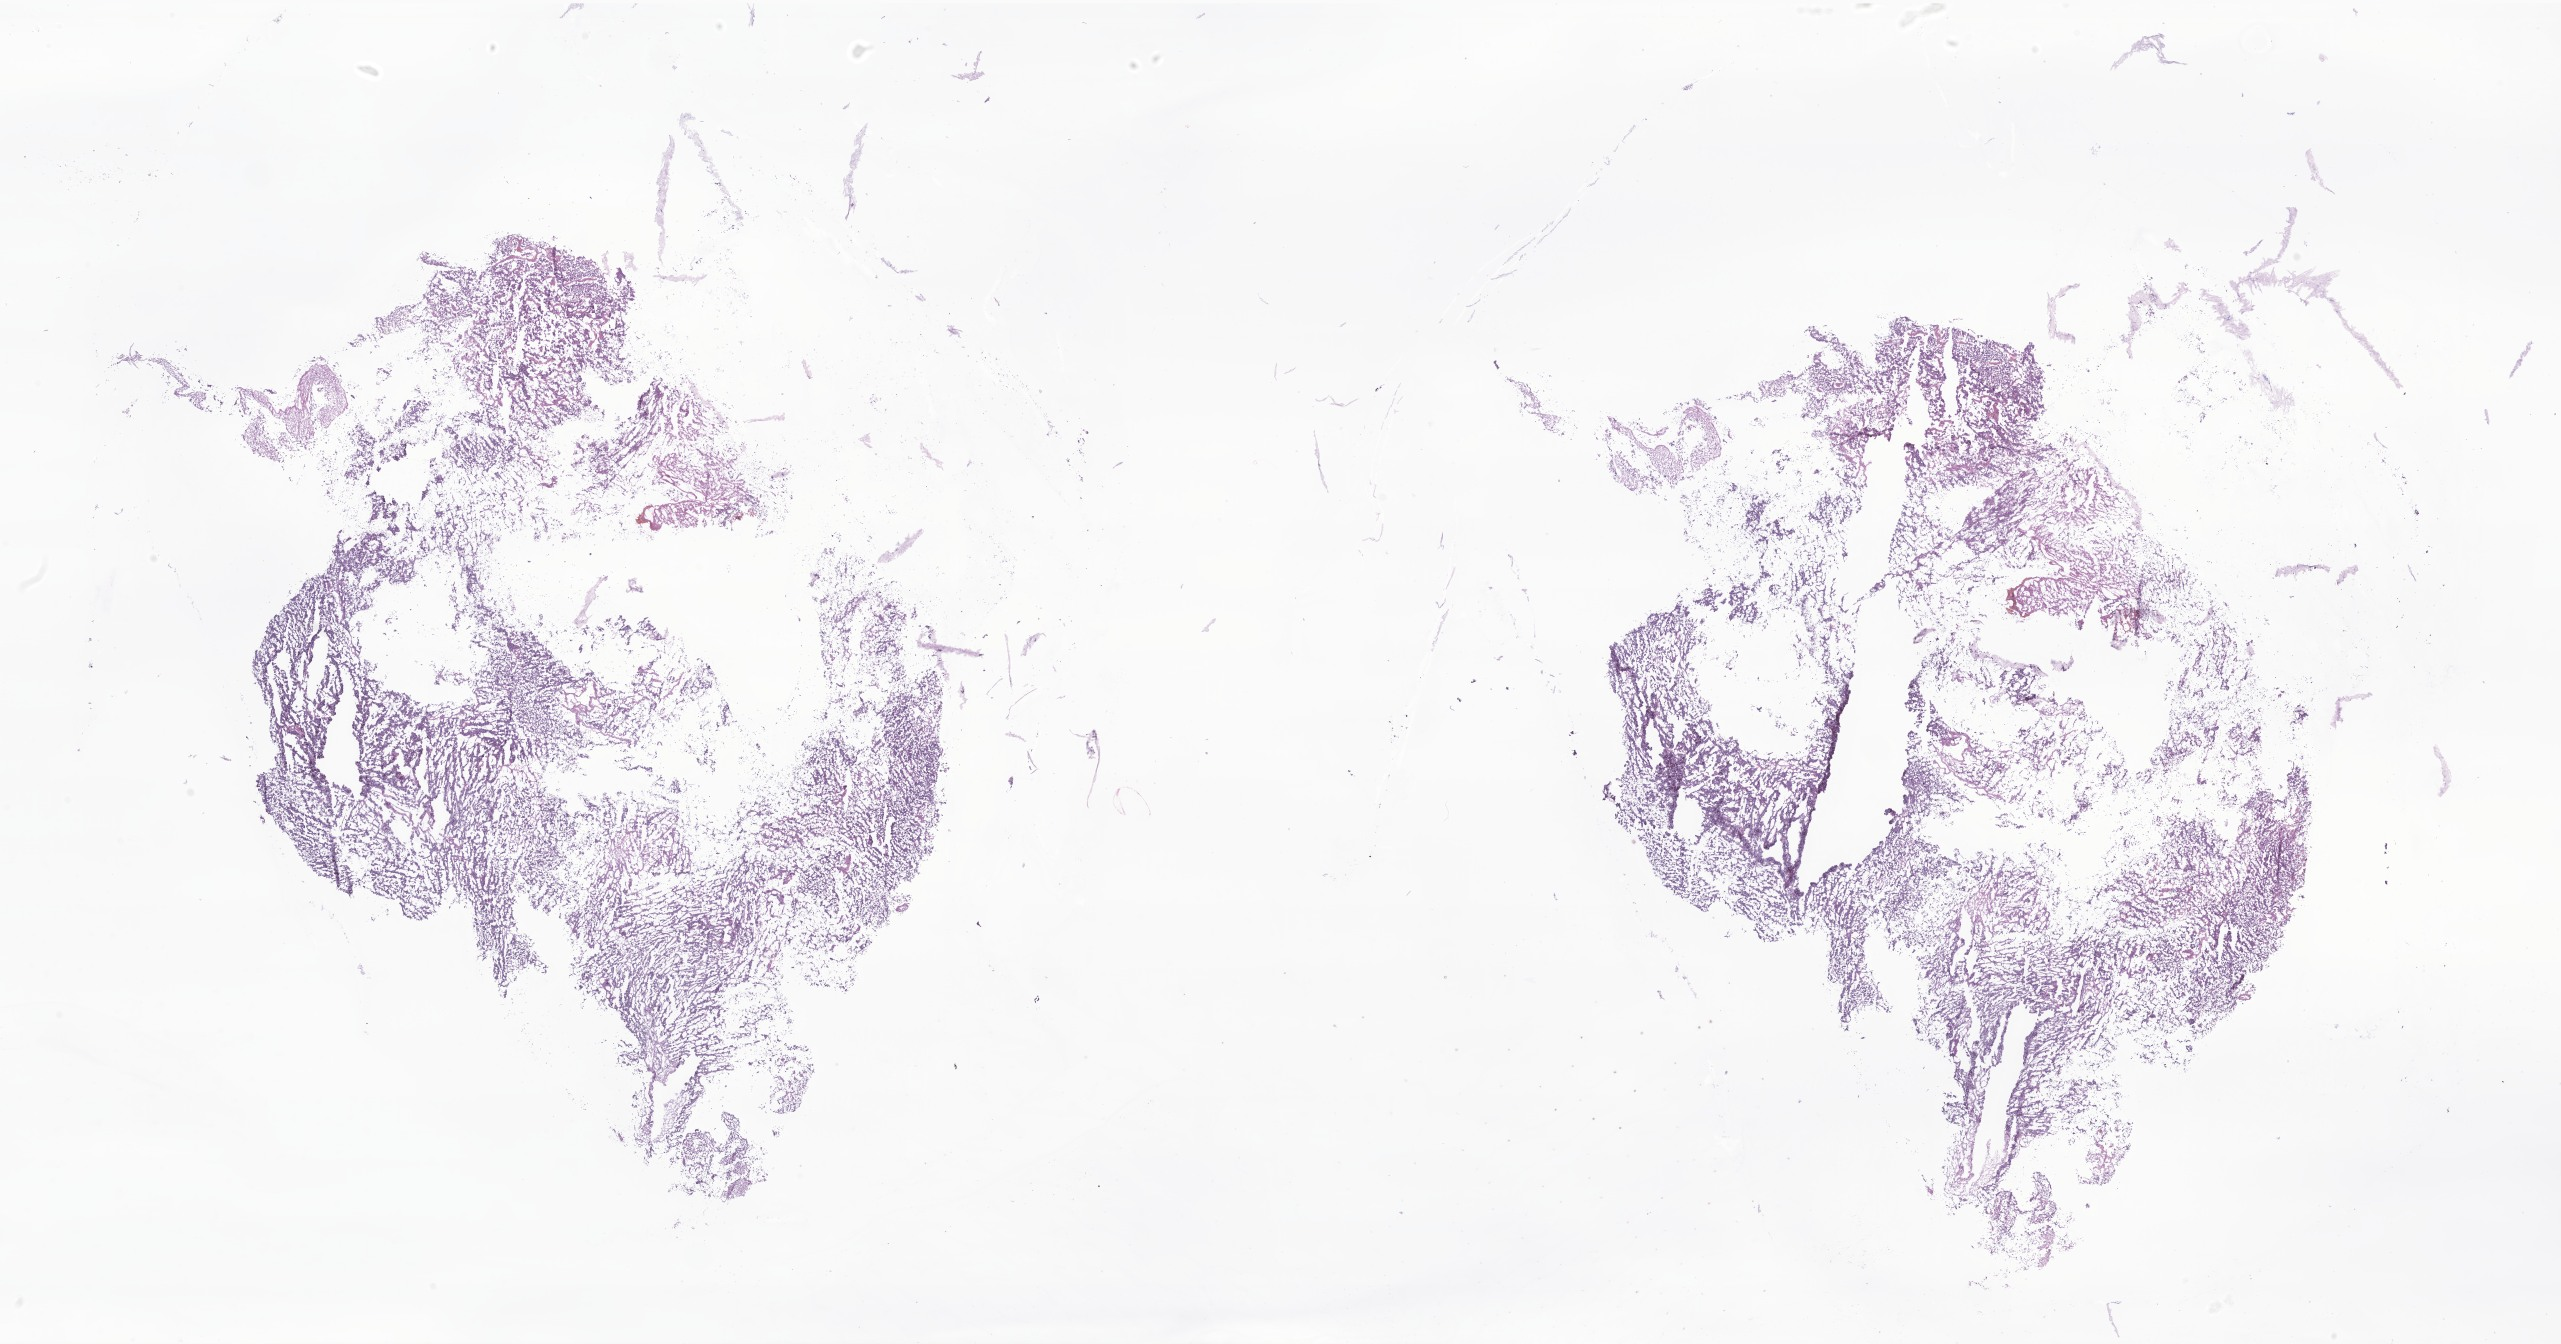
Whole-slide image, H&E stain of tumor tissue from the brain, low-resolution overview of the scanned area, about 43.2 x 22.7 mm; frozen section (OCT-embedded). Patient: male, age 38 months (3 years 2 months).
Recorded diagnosis: CNS embryonal tumor, NOS.